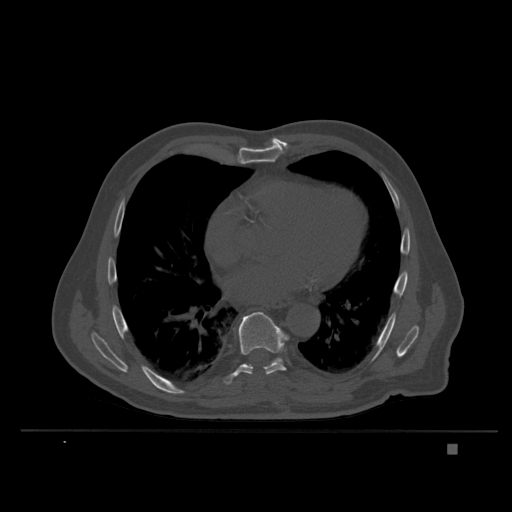
CT including the spine, one axial slice; position 228 of 435 along the scan axis; bone window (W 1800 / L 400 HU); 1.5 mm slice thickness; 512 × 512 image matrix. Patient: male, 73 years. Case-level facts recorded for this patient, not image findings: primary cancer: skin.
Outlined on this slice (semi-automatic segmentation, software-assisted and operator-edited):
- T8 vertebra: bounding box <224,312,290,385> (left, top, right, bottom; pixels)
- T9 vertebra: <268,358,280,366>